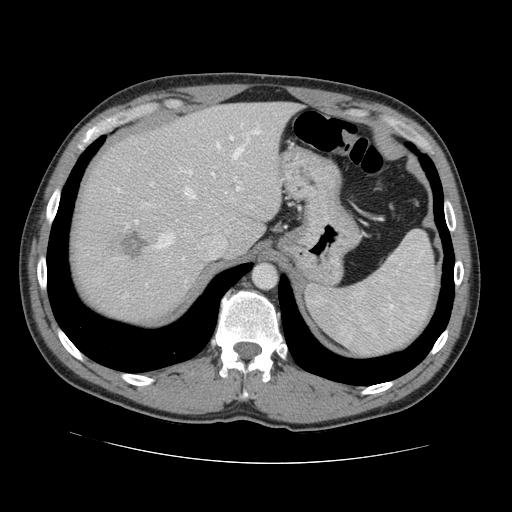
Contrast-enhanced abdominal CT, one axial slice; intravenous contrast given; soft-tissue window (W 400 / L 40 HU); 512 × 512 image matrix. Male patient, age 40 years. Case-level facts recorded for this patient, not image findings: diagnosis: colorectal cancer liver metastases, imaged before liver resection; multiple liver metastases: yes; largest metastasis: 2.9 cm; disease in both lobes: yes.
Structures marked on this image (outlined manually by an expert reader):
- hepatic veins: bounding box <156,143,243,248> (left, top, right, bottom; pixels)
- liver: <73,104,293,321>
- planned liver remnant (the part of the liver to remain after resection): <100,103,294,256>
- portal vein (with intrahepatic branches): <189,132,260,191>
- liver metastasis: <118,231,148,260>